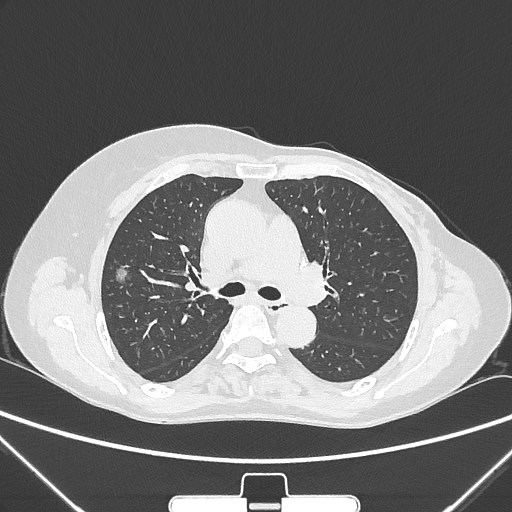
Chest CT, one axial slice; slice 162 of 265 in the series (ordered by position); reconstruction kernel IMR1,SharpPlus; lung window (W 1500 / L -600 HU); 512 × 512 image matrix, field of view 350 × 350 mm. Female patient, age 64 years. From the clinical record (not read from this slice): clinical TNM (as recorded): T1c N0 M0; histopathological grade: G1-2.
Outlined on this slice (rectangle marked by the reading radiologist):
- lung tumour (recorded histology: adenocarcinoma): bounding box [x1, y1, x2, y2] px = [110, 260, 133, 289]